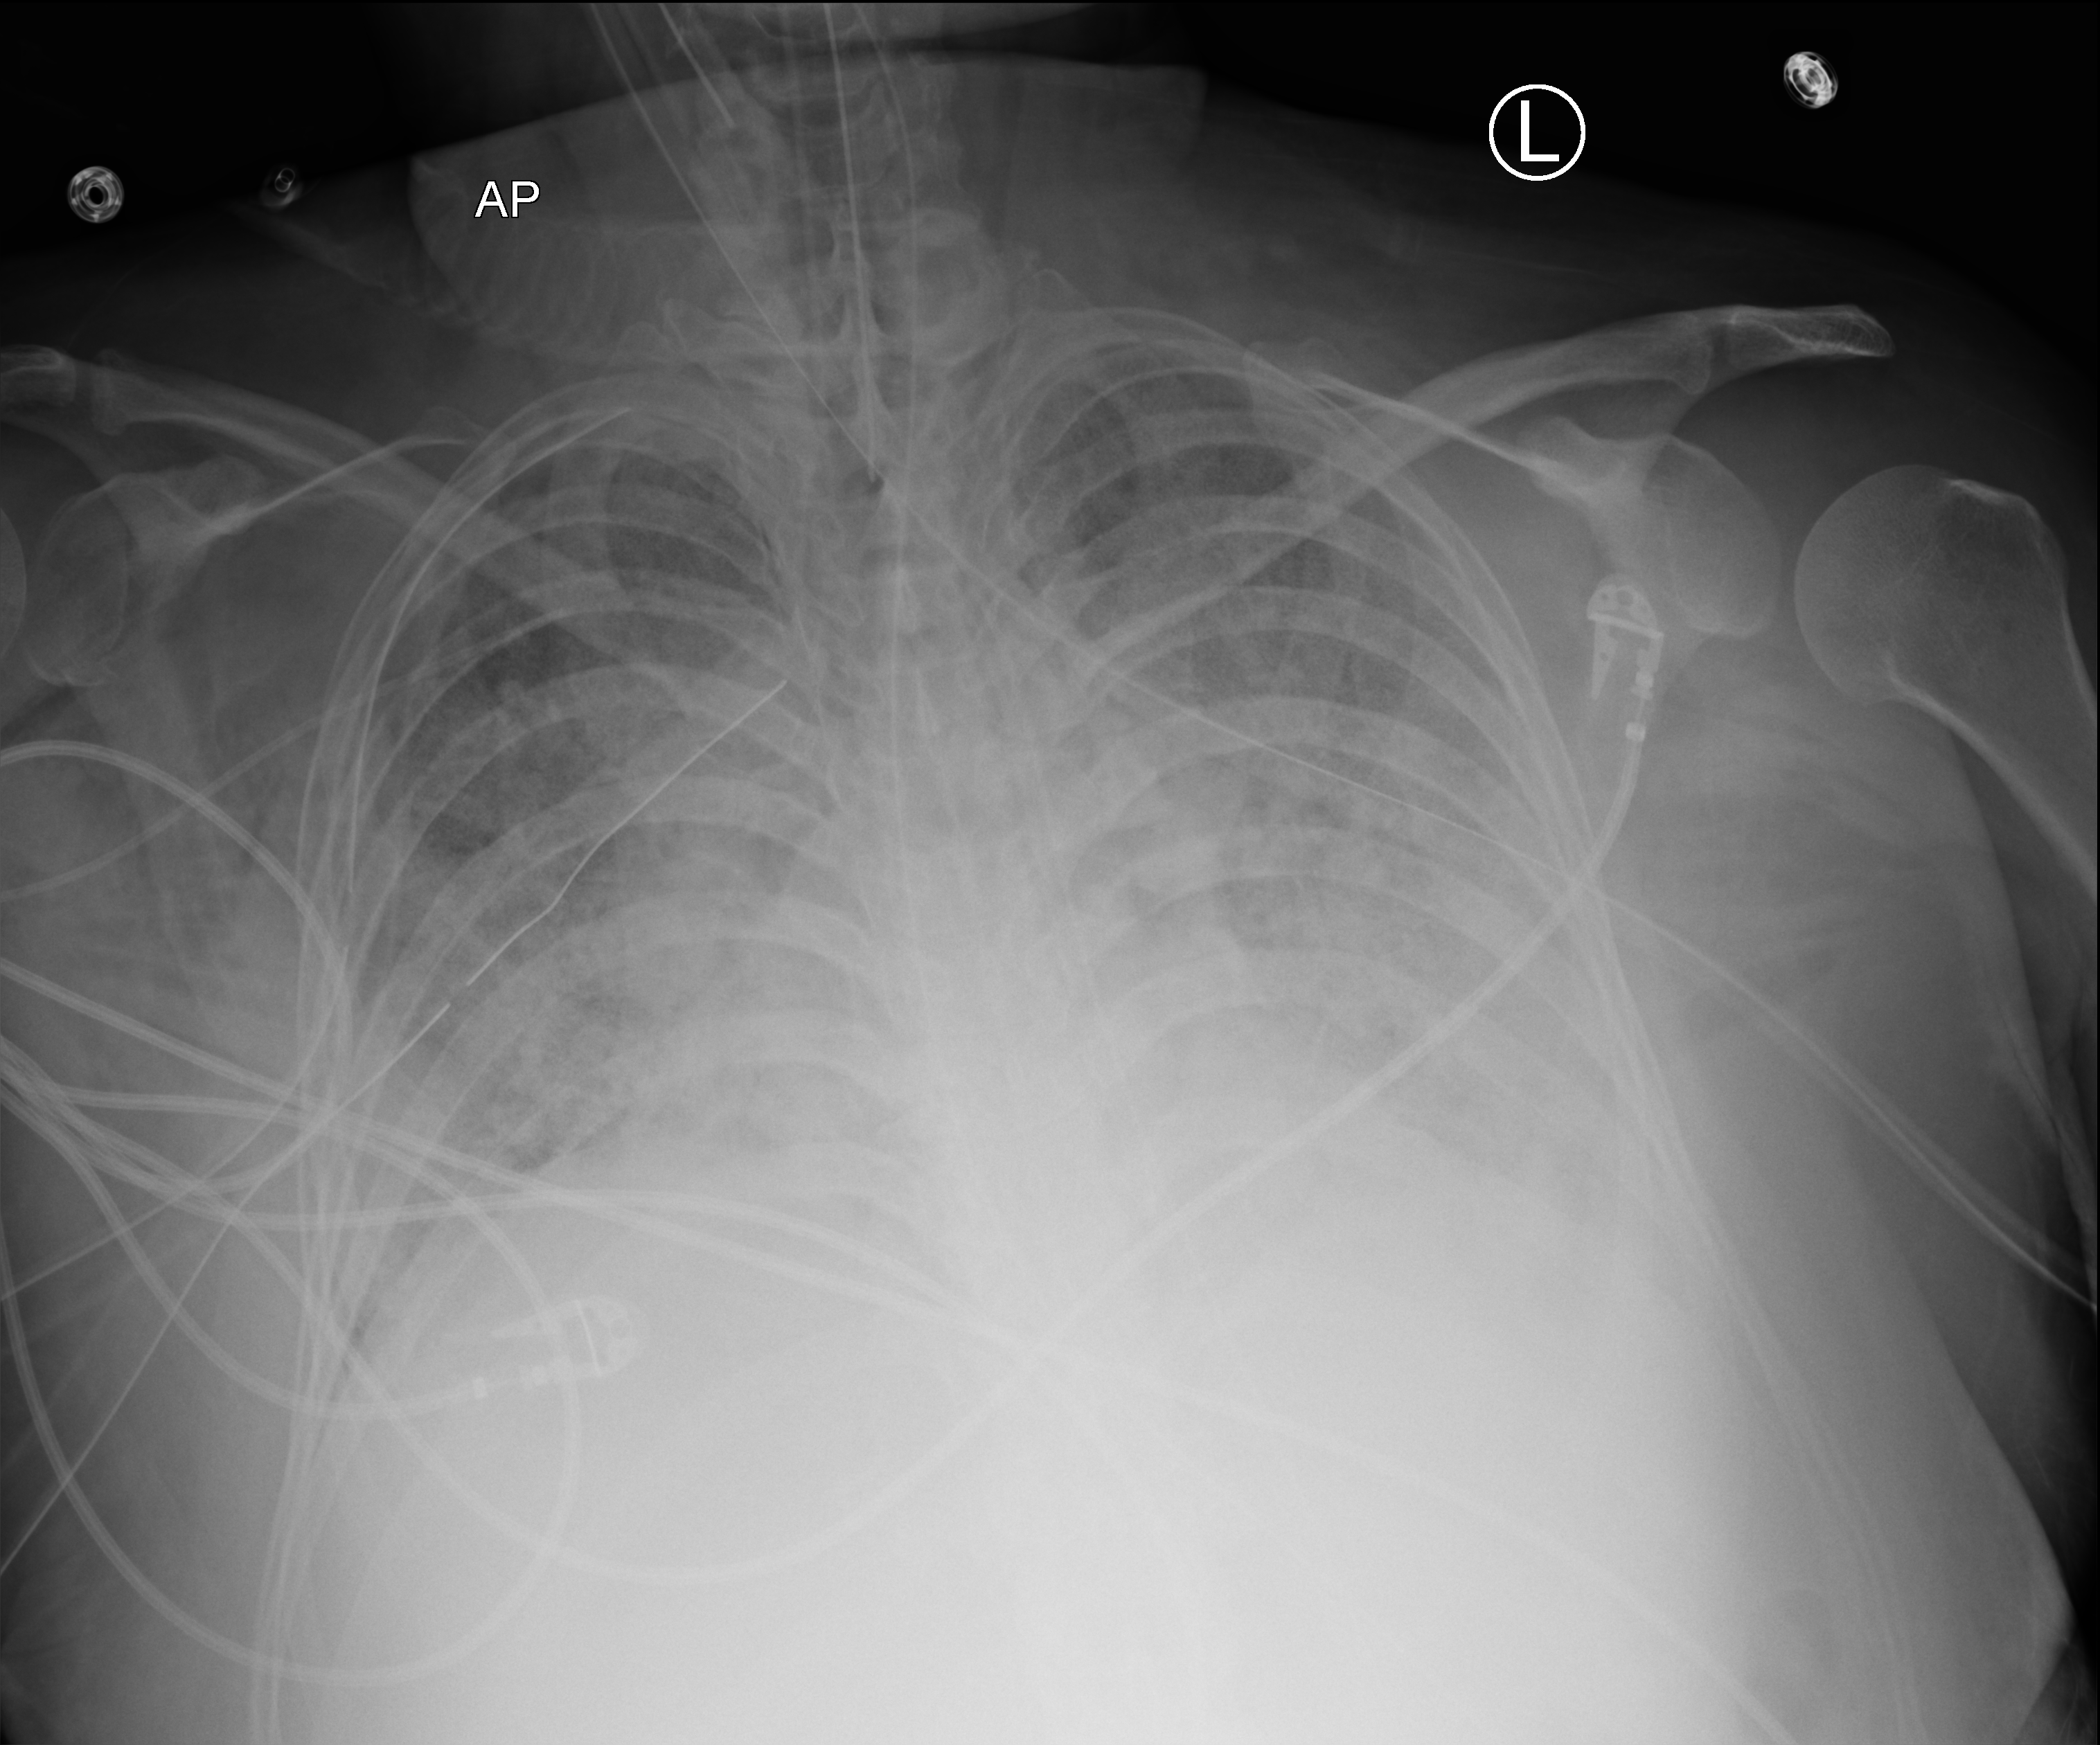
Chest X-ray (portable); anteroposterior (AP) projection. Patient hospitalised with COVID-19, aged 18–59 years.
From the hospital-stay record, not from the radiograph (when in the stay this image was taken is not recorded): admitted to intensive care during this hospital stay: yes.